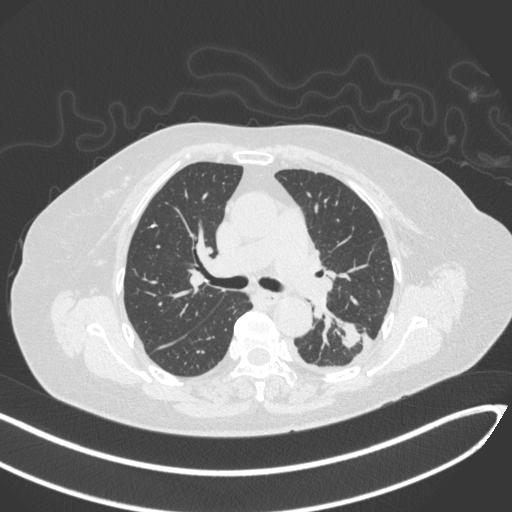
Chest CT, one axial slice. Position 197 of 270 along the scan axis. Reconstruction kernel B31f. Lung window (W 1500 / L -600 HU). 512 × 512 image matrix. Female patient, age 76 years. Case-level facts recorded for this patient, not image findings: clinical TNM (as recorded): T1c N0 M0.
Outlined on this slice (rectangle marked by the reading radiologist):
- lung tumour (recorded histology: adenocarcinoma): box from (x=335, y=320) to (x=361, y=349) px